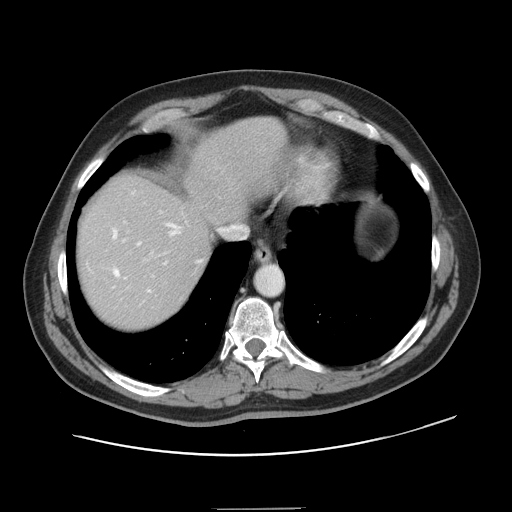
Contrast-enhanced abdominal CT, one axial slice; slice 125 of 143 in the series (ordered by position); intravenous contrast given; soft-tissue window (W 400 / L 40 HU); 2.5 mm slice thickness; 512 × 512 image matrix, field of view 402 × 402 mm. Male patient, age 62 years. From the clinical record (not read from this slice): diagnosis: colorectal cancer liver metastases, imaged before liver resection; multiple liver metastases: yes; largest metastasis: 2.7 cm; chemotherapy before resection: yes.
Structures marked on this image (manually delineated by an expert):
- hepatic veins: box from (x=113, y=223) to (x=200, y=292) px
- liver: (x=77, y=117)–(x=287, y=330)
- planned liver remnant (the part of the liver to remain after resection): (x=77, y=117)–(x=287, y=296)
- portal vein (with intrahepatic branches): (x=123, y=222)–(x=153, y=253)